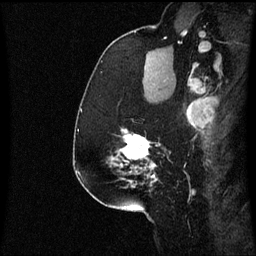
Breast MRI (dynamic contrast-enhanced), one sagittal slice; slice 43 of 60 in the series (ordered by position); dynamic contrast-enhanced series, image 2 of 3 at this slice position (ordered by acquisition); 1.5 T; TE 4.2 ms, TR 8.9 ms; 256 × 256 image matrix. Female patient, age 58 years. Case-level facts recorded for this patient, not image findings: setting: breast cancer imaged before/during neoadjuvant chemotherapy; receptor status: triple-negative.
Structures marked on this image (semi-automatic segmentation, software-assisted and operator-edited):
- analysis volume of interest (the breast-tissue region the enhancement analysis was run in; not a lesion): bounding box <108,128,171,179> (left, top, right, bottom; pixels)
- tumour enhancement mask (voxels above the 70 % enhancement threshold inside the analysis volume of interest): <120,130,157,179>